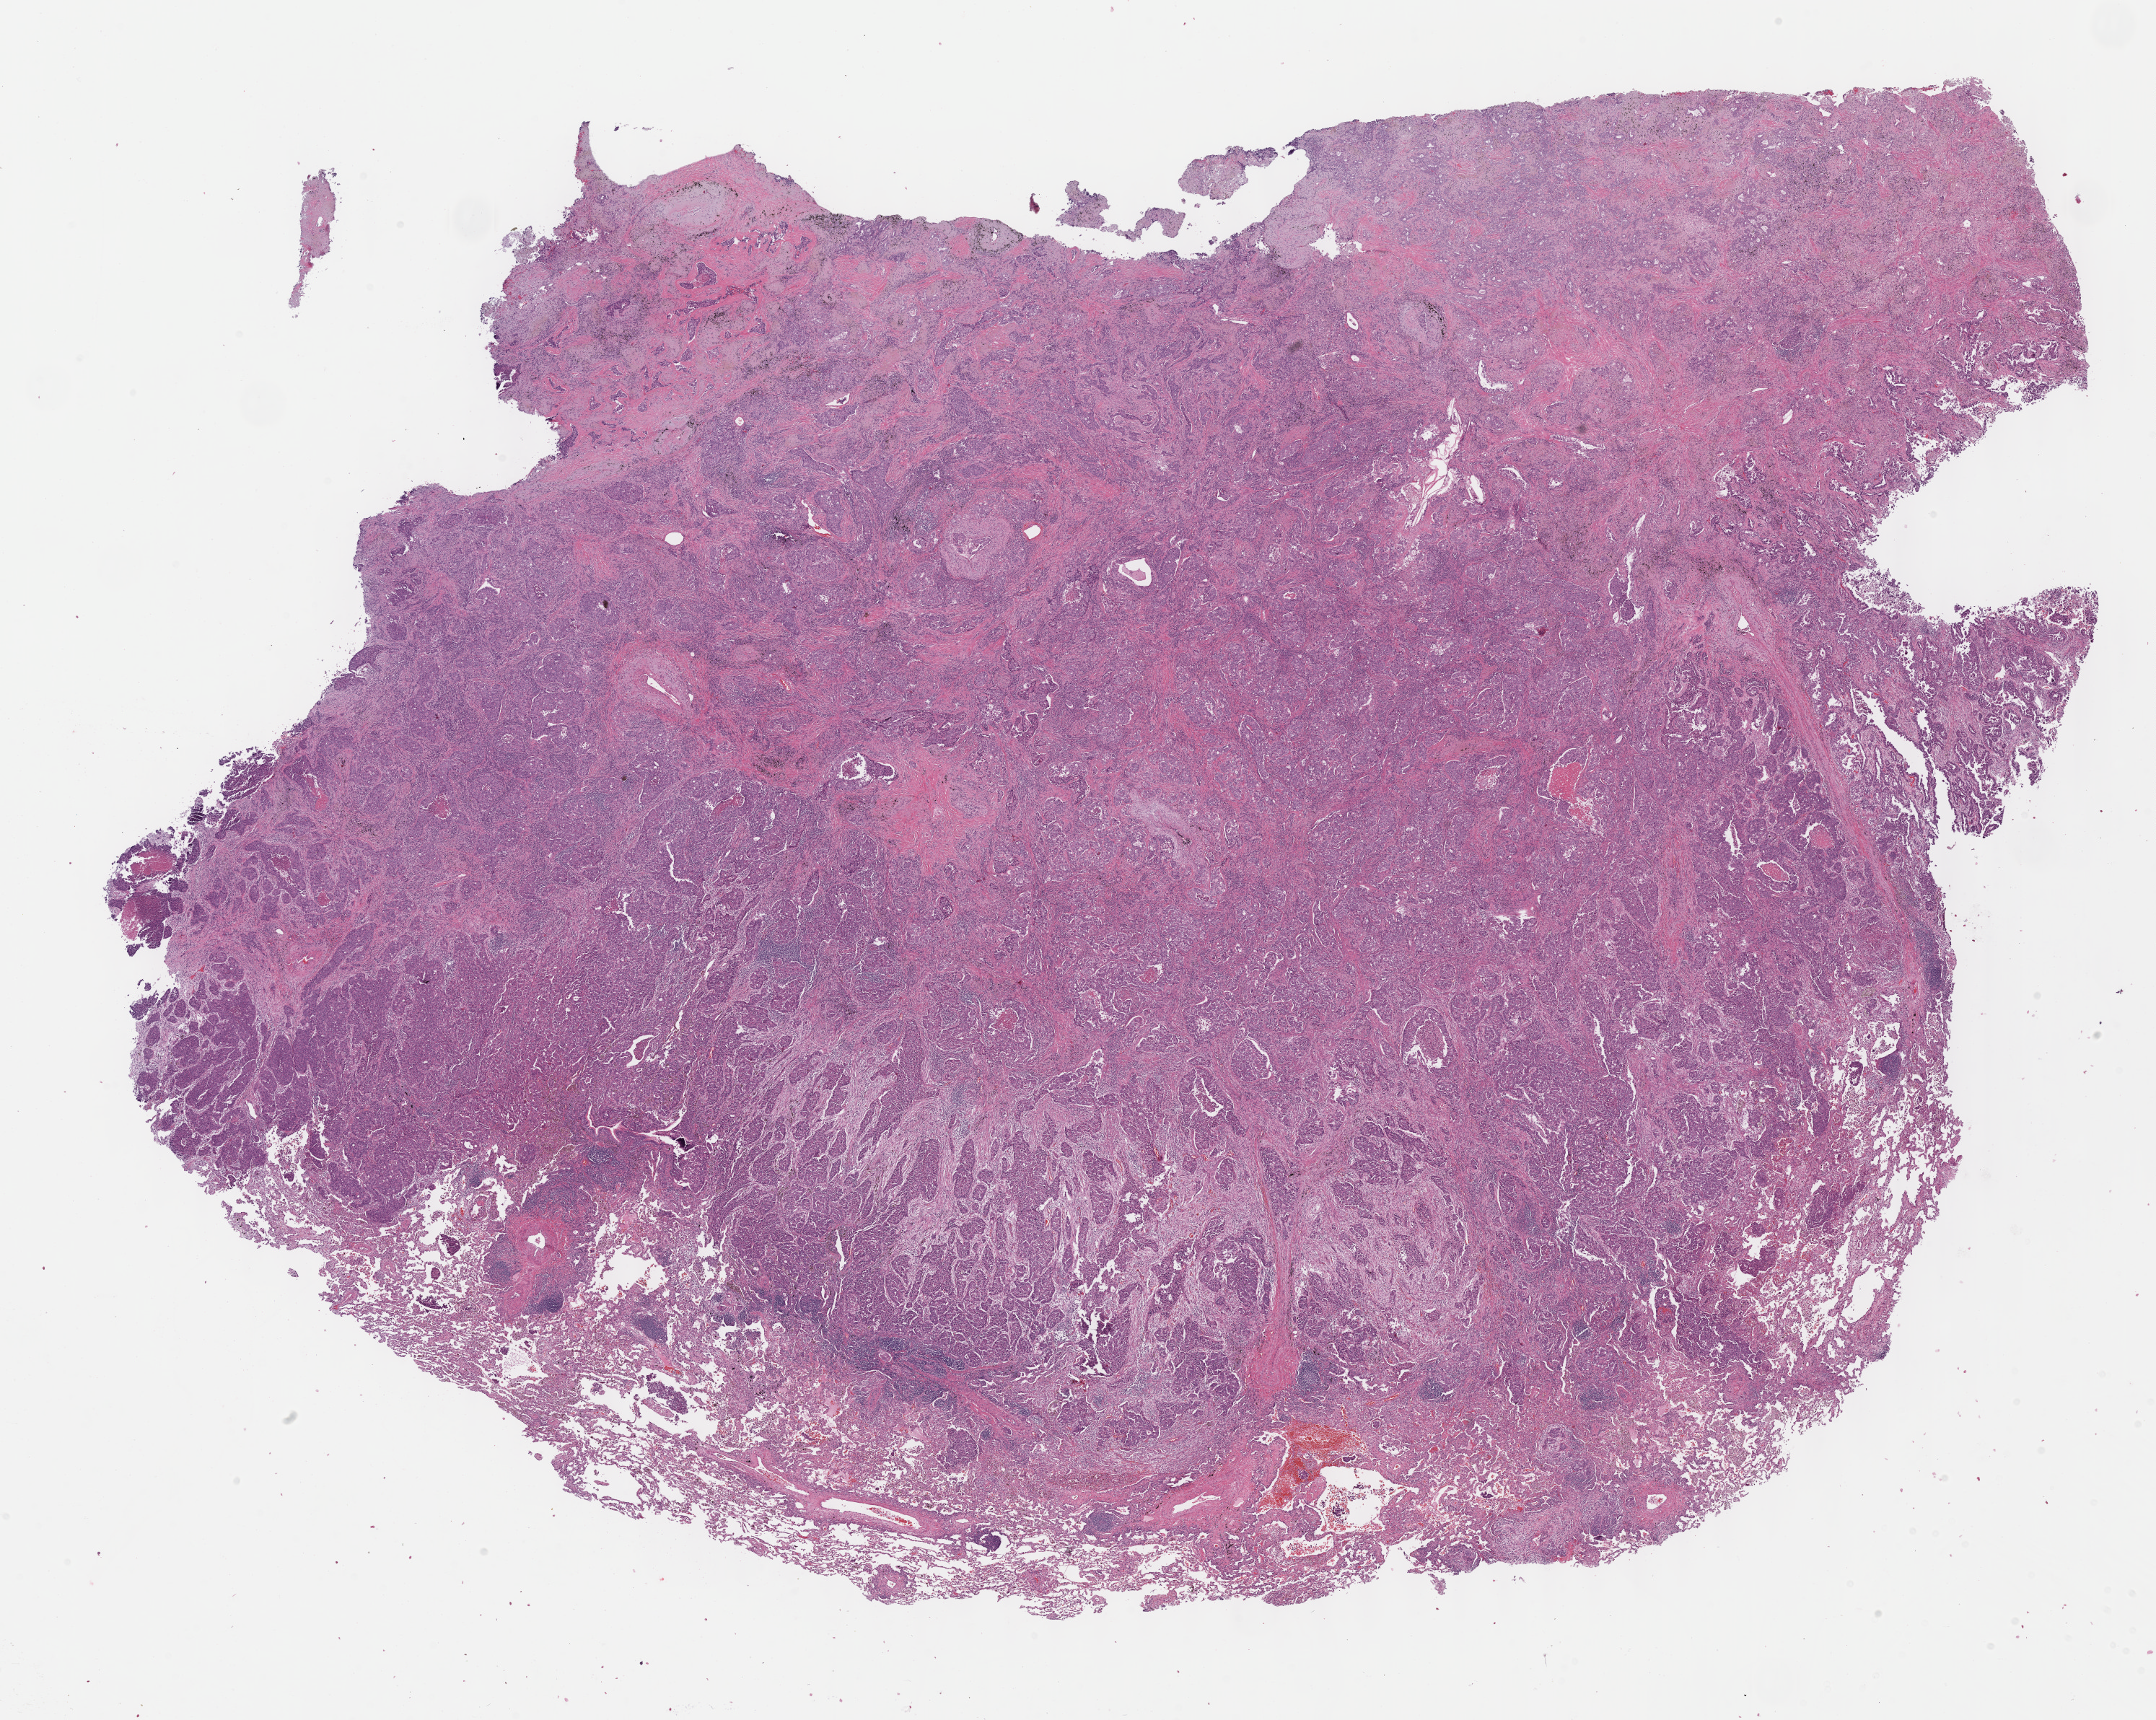
Whole-slide histology image, H&E-stained — shown as a low-resolution overview of the whole scanned area (about 24.1 x 19.3 mm), FFPE section, sample: primary tumour, lung. Female patient; age at initial diagnosis 60 years.
- diagnosis: Squamous cell carcinoma, NOS (upper lobe, lung)
- AJCC pathologic stage: IIIA
- laterality: left